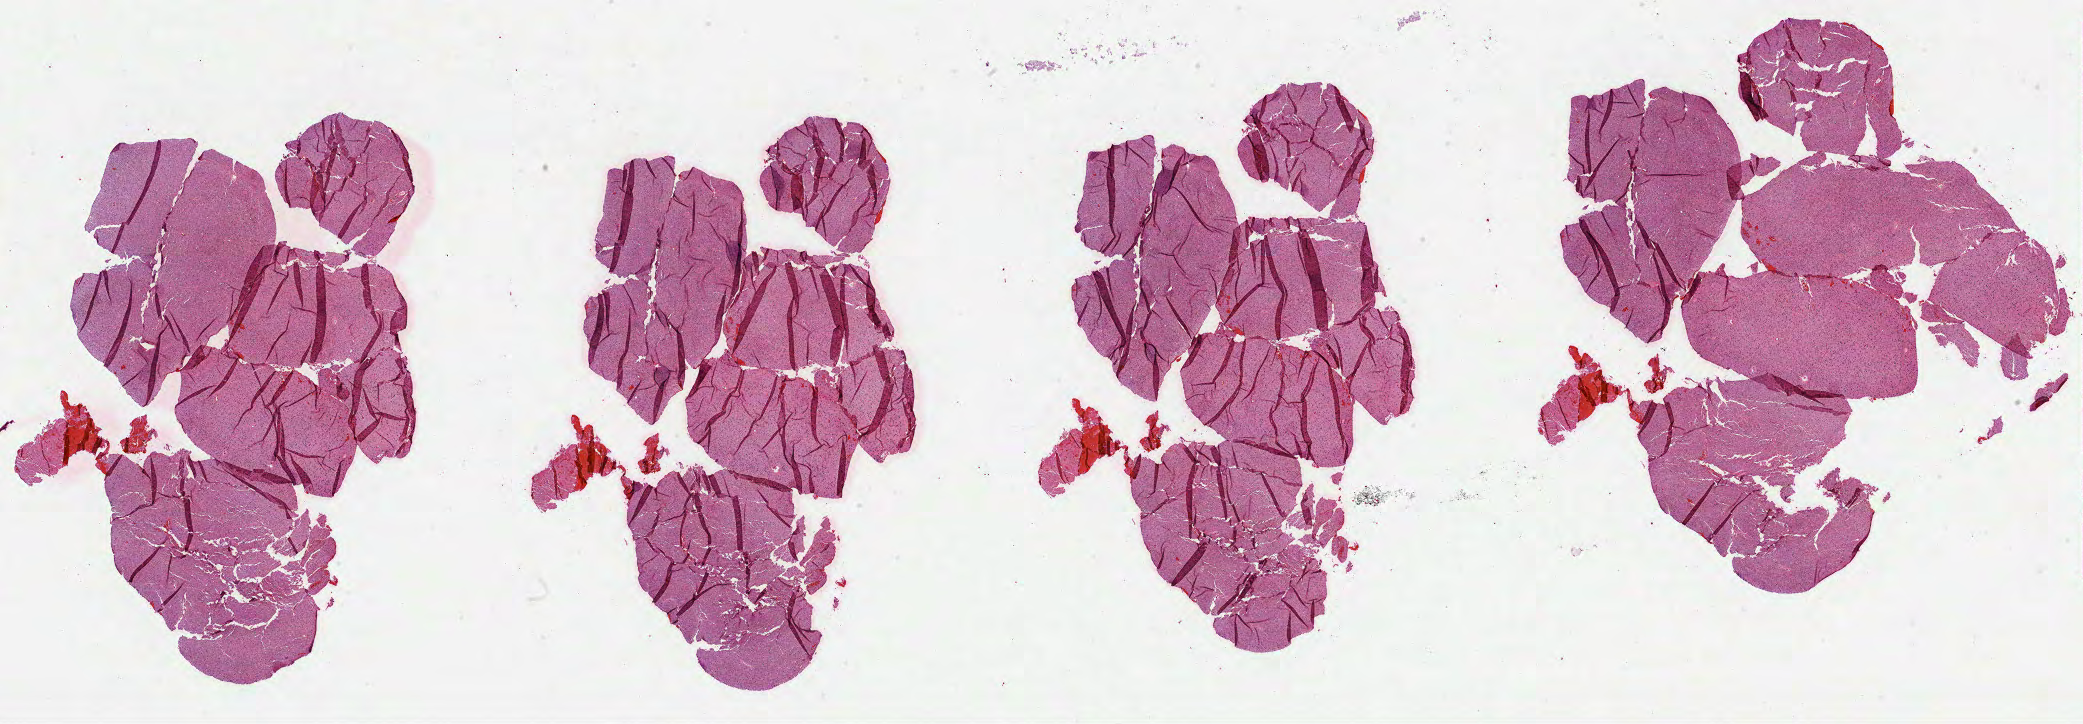
Whole-slide histology image, H&E-stained, shown as a low-resolution overview of the whole scanned area (about 33.6 x 11.7 mm, slide scanned at 40x); FFPE section; sample: primary tumour, brain. Patient: female, age at initial diagnosis 26 years. Histologic grade: G2 (moderately differentiated).
Diagnosis: Oligodendroglioma, NOS.